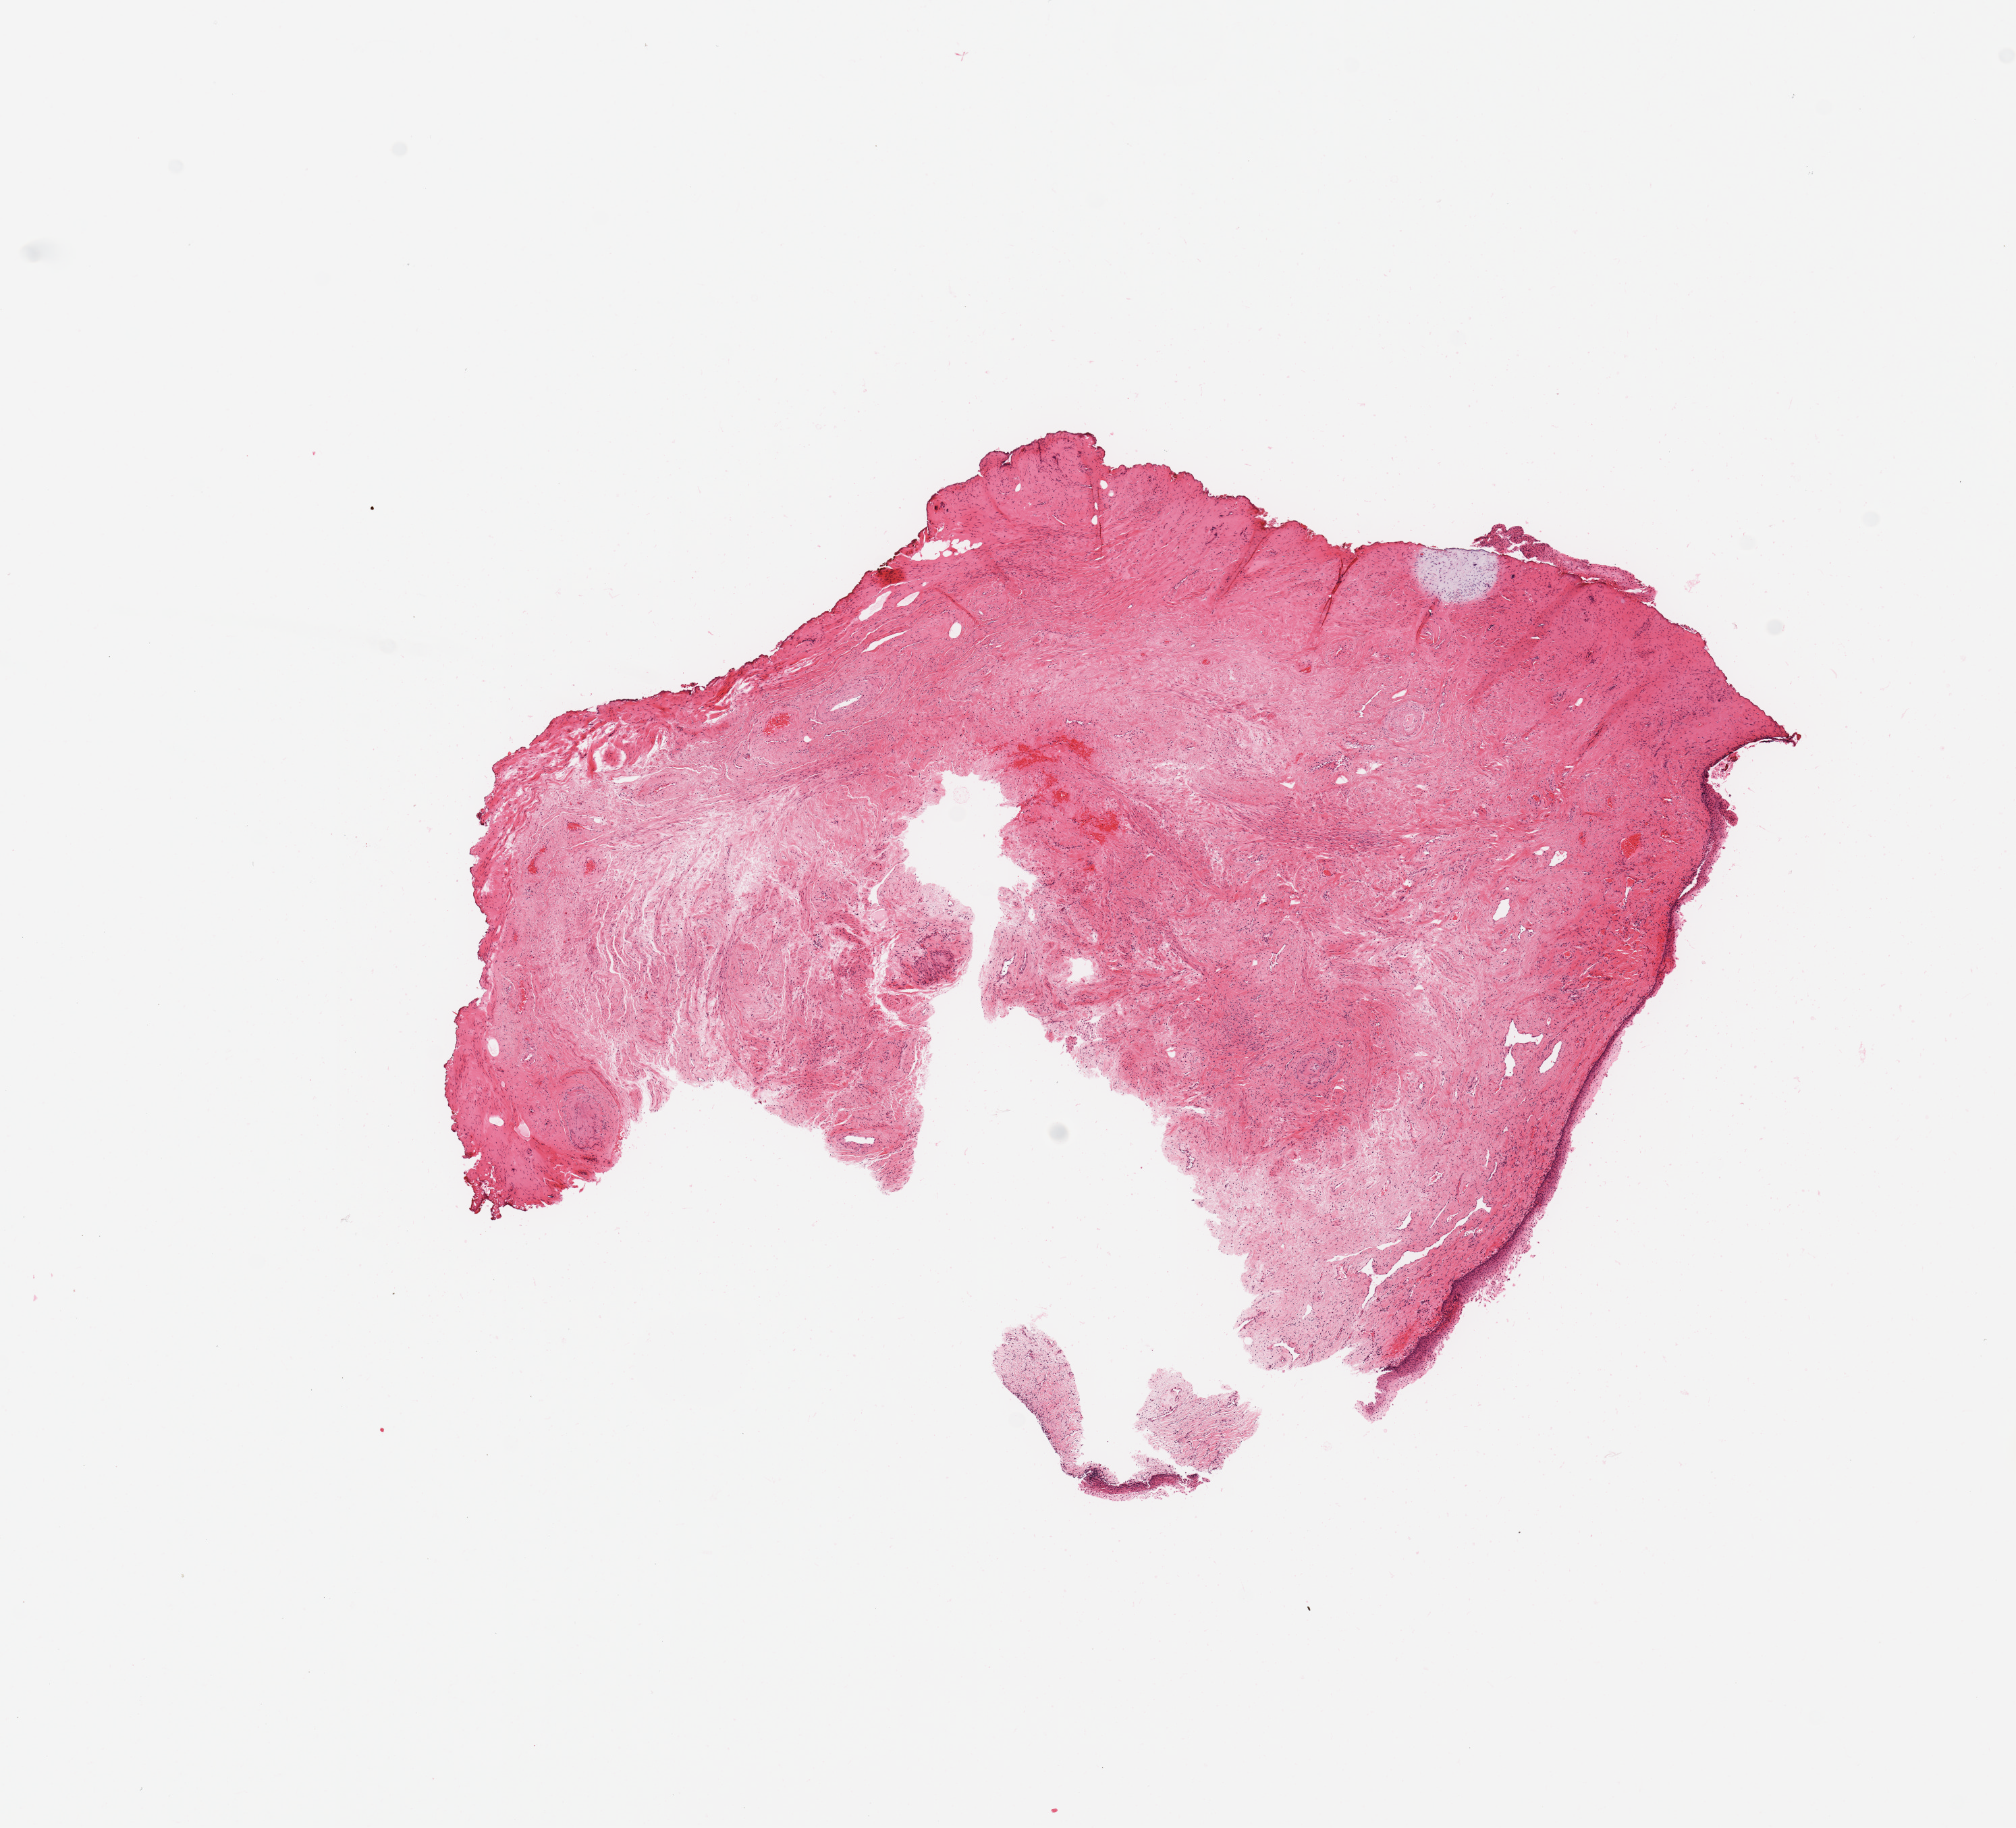
Digitized H&E-stained tissue section (whole slide), a low-resolution overview of the entire scanned area, about 11.8 x 10.7 mm. Normal (non-tumour) tissue sample, uterus. 73-year-old female patient.
This section: normal (non-tumour) tissue from the same patient. Patient diagnosis: Endometrioid adenocarcinoma, NOS.